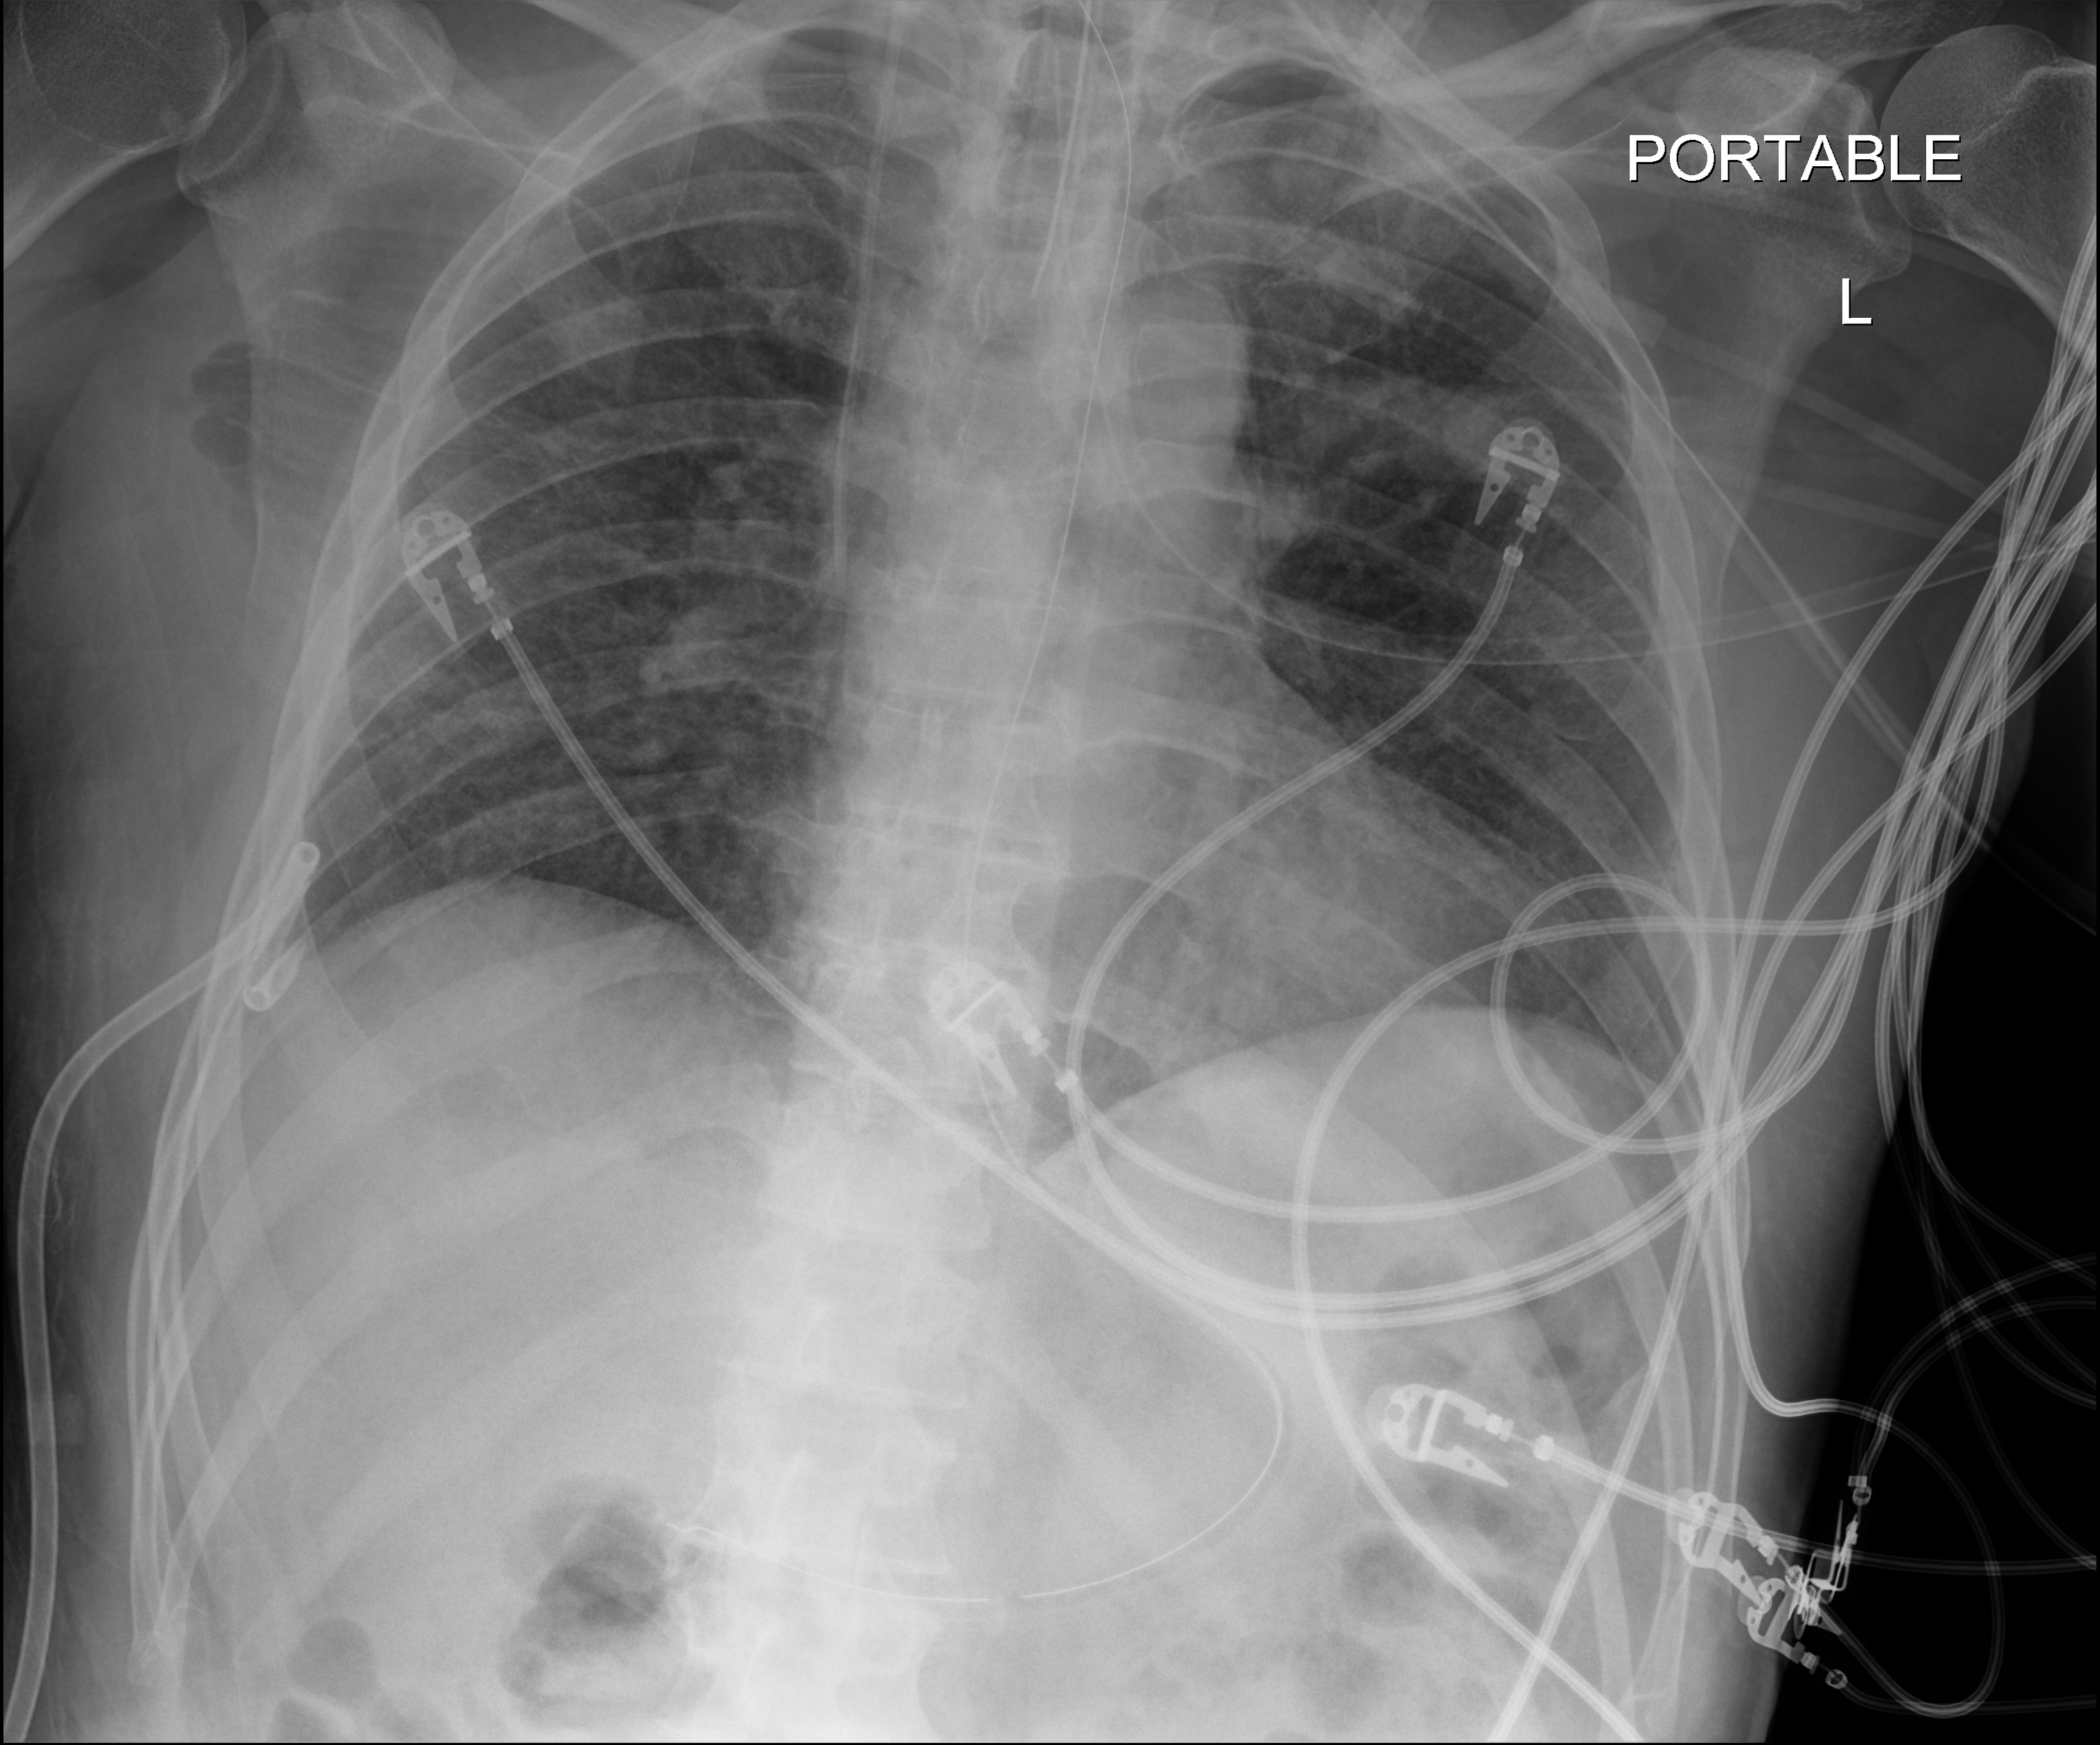
Portable chest radiograph; anteroposterior (AP) projection. Male patient hospitalised with COVID-19, age 18–59 years.
From the hospital-stay record, not from the radiograph (when in the stay this image was taken is not recorded): chronic kidney disease (admission record): no.